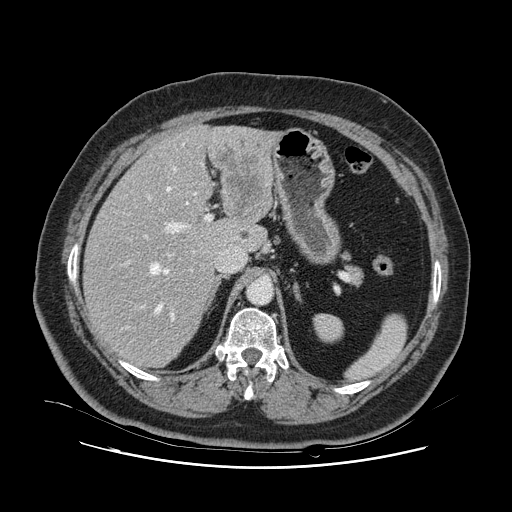
Contrast-enhanced abdominal CT, one axial slice. Position 73 of 132 along the scan axis. 120 kVp. Intravenous contrast given. Soft-tissue window (W 400 / L 40 HU). 2.5 mm slice thickness. 512 × 512 image matrix, field of view 391 × 391 mm. Female patient, age 73 years. From the clinical record (not read from this slice): diagnosis: colorectal cancer liver metastases, imaged before liver resection; multiple liver metastases: no; largest metastasis: 7 cm; disease in both lobes: no.
Annotated regions visible in this slice (expert manual segmentation):
- hepatic veins: bounding box <150,145,197,312> (left, top, right, bottom; pixels)
- liver: <84,127,273,368>
- planned liver remnant (the part of the liver to remain after resection): <85,156,241,367>
- portal vein (with intrahepatic branches): <125,196,212,321>
- liver metastasis: <241,233,250,240>
- liver metastasis: <216,140,261,215>